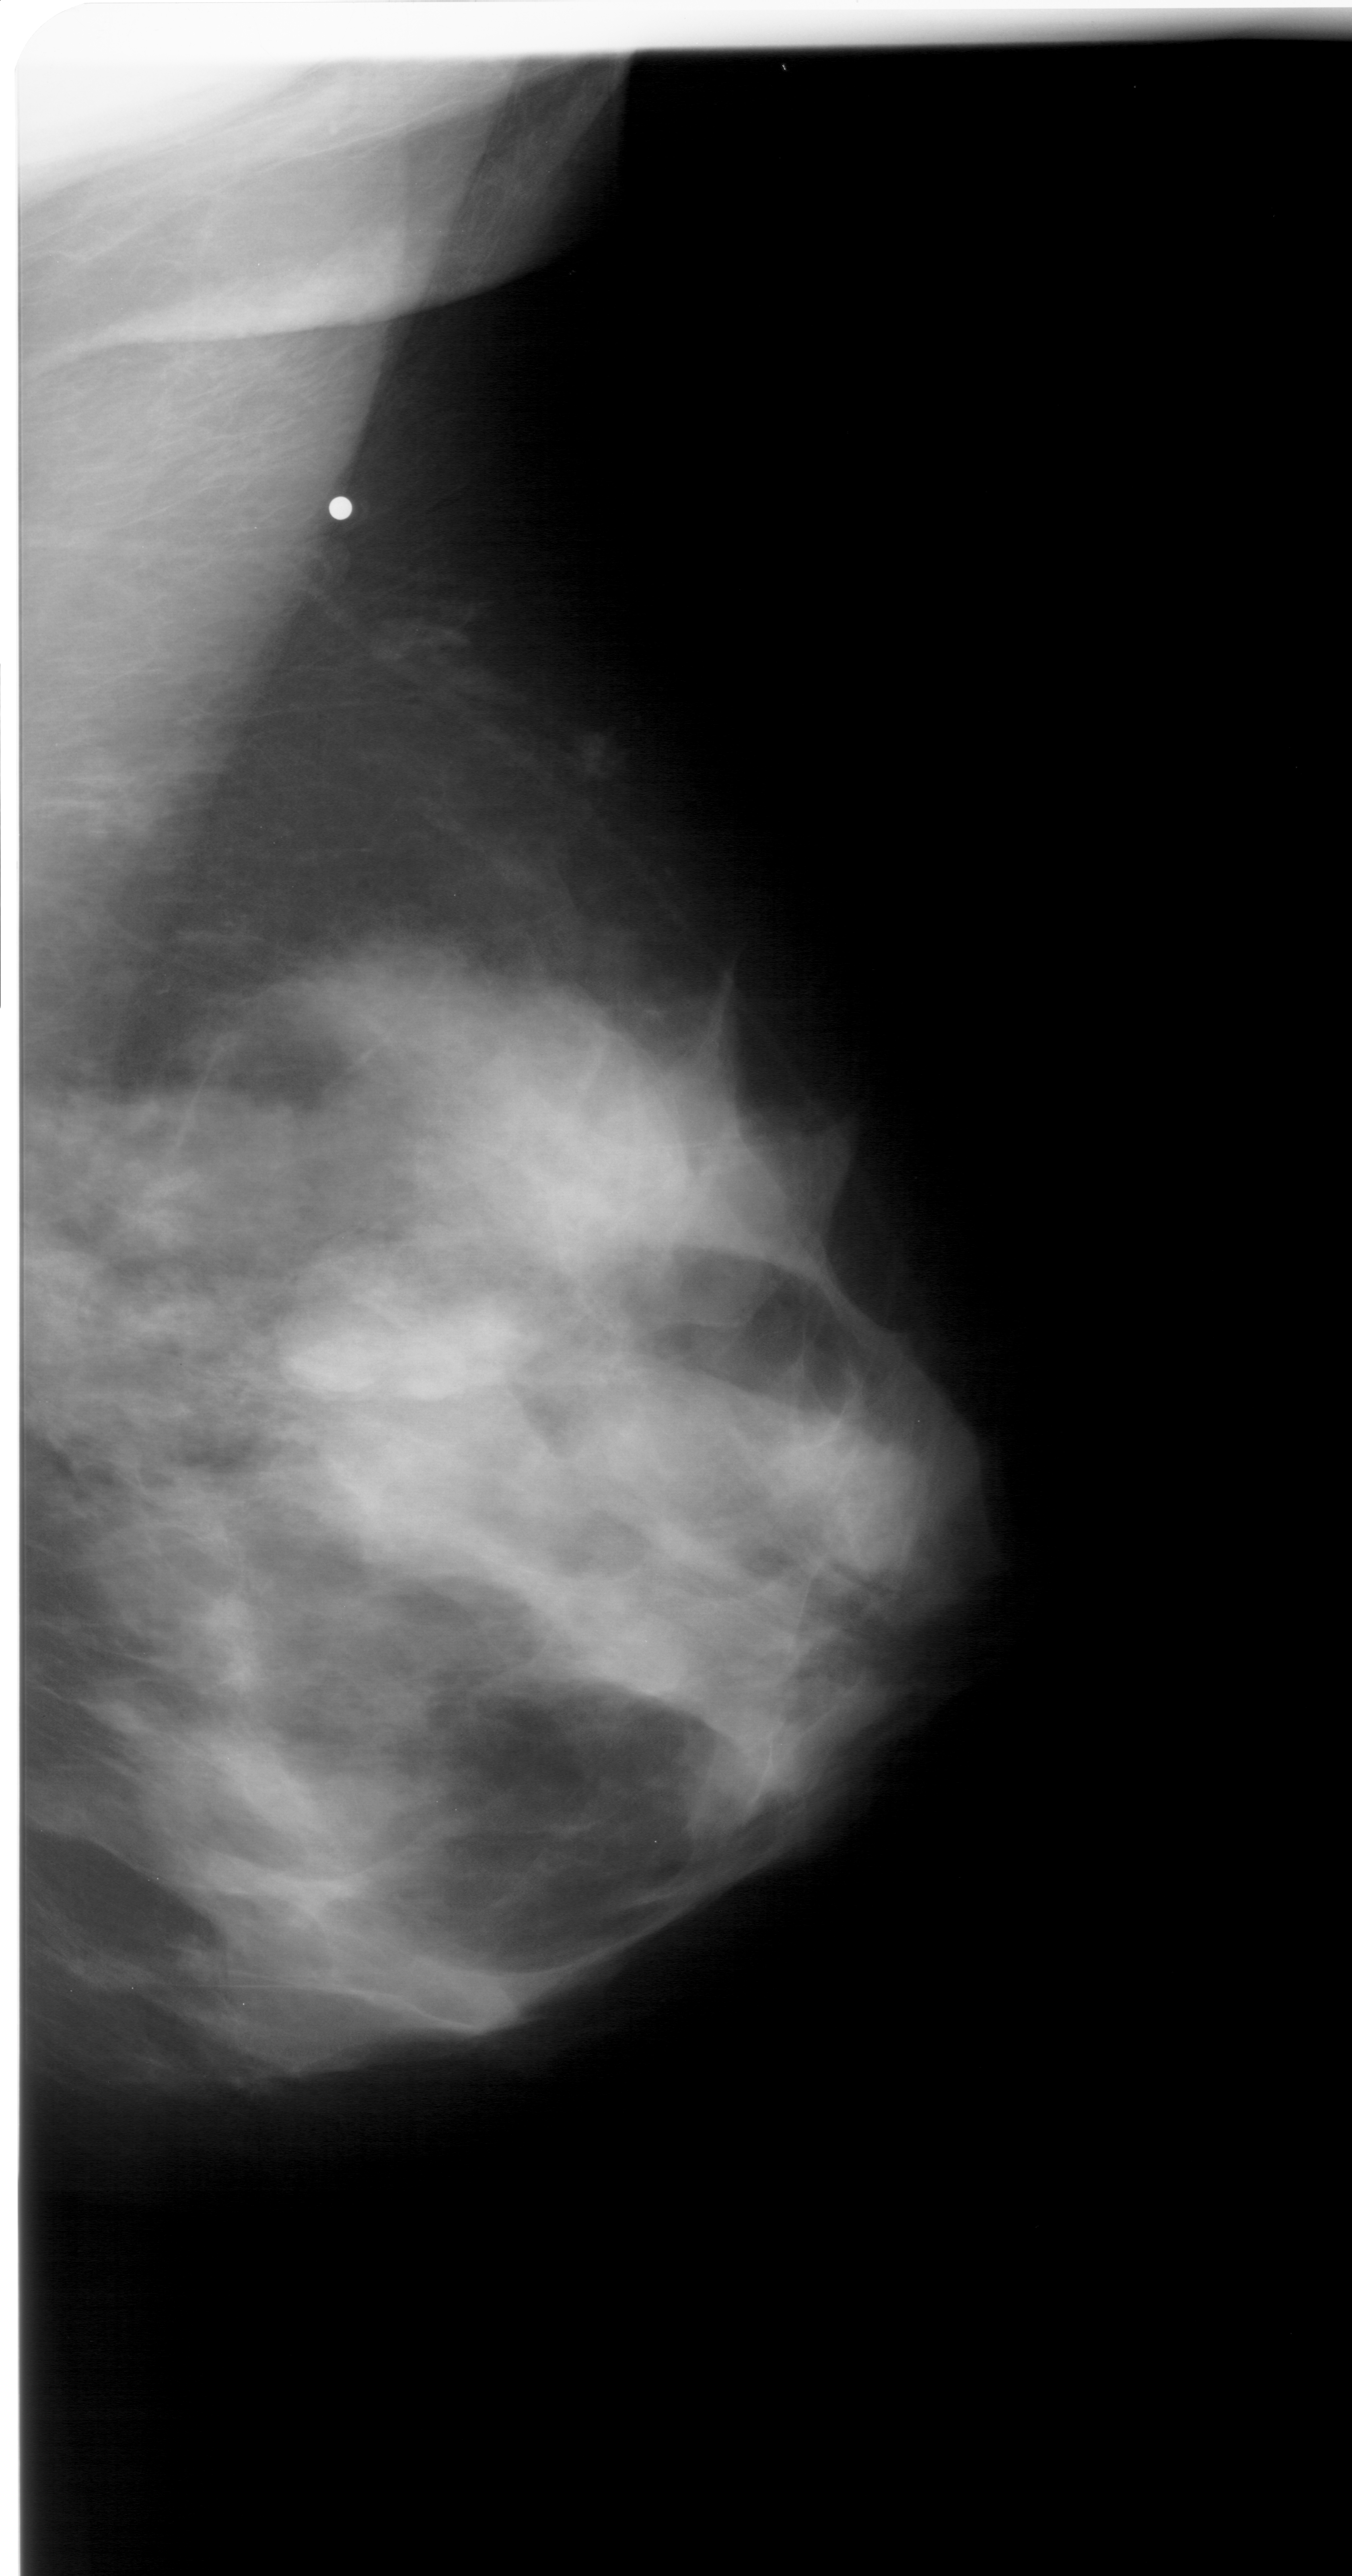
Scanned film-screen mammogram; right breast; MLO view; BI-RADS breast density category 4 (scale 1–4); 1352 × 2576 image matrix.
Marked abnormalities (boxes around the expert regions of interest):
- mass, shape lobulated, margins obscured; BI-RADS assessment category 4; subtlety rating 3 on a 1 (subtle) to 5 (obvious) scale; pathology result (as recorded, not read from the image): benign: bounding box [x1, y1, x2, y2] px = [296, 1271, 512, 1406]